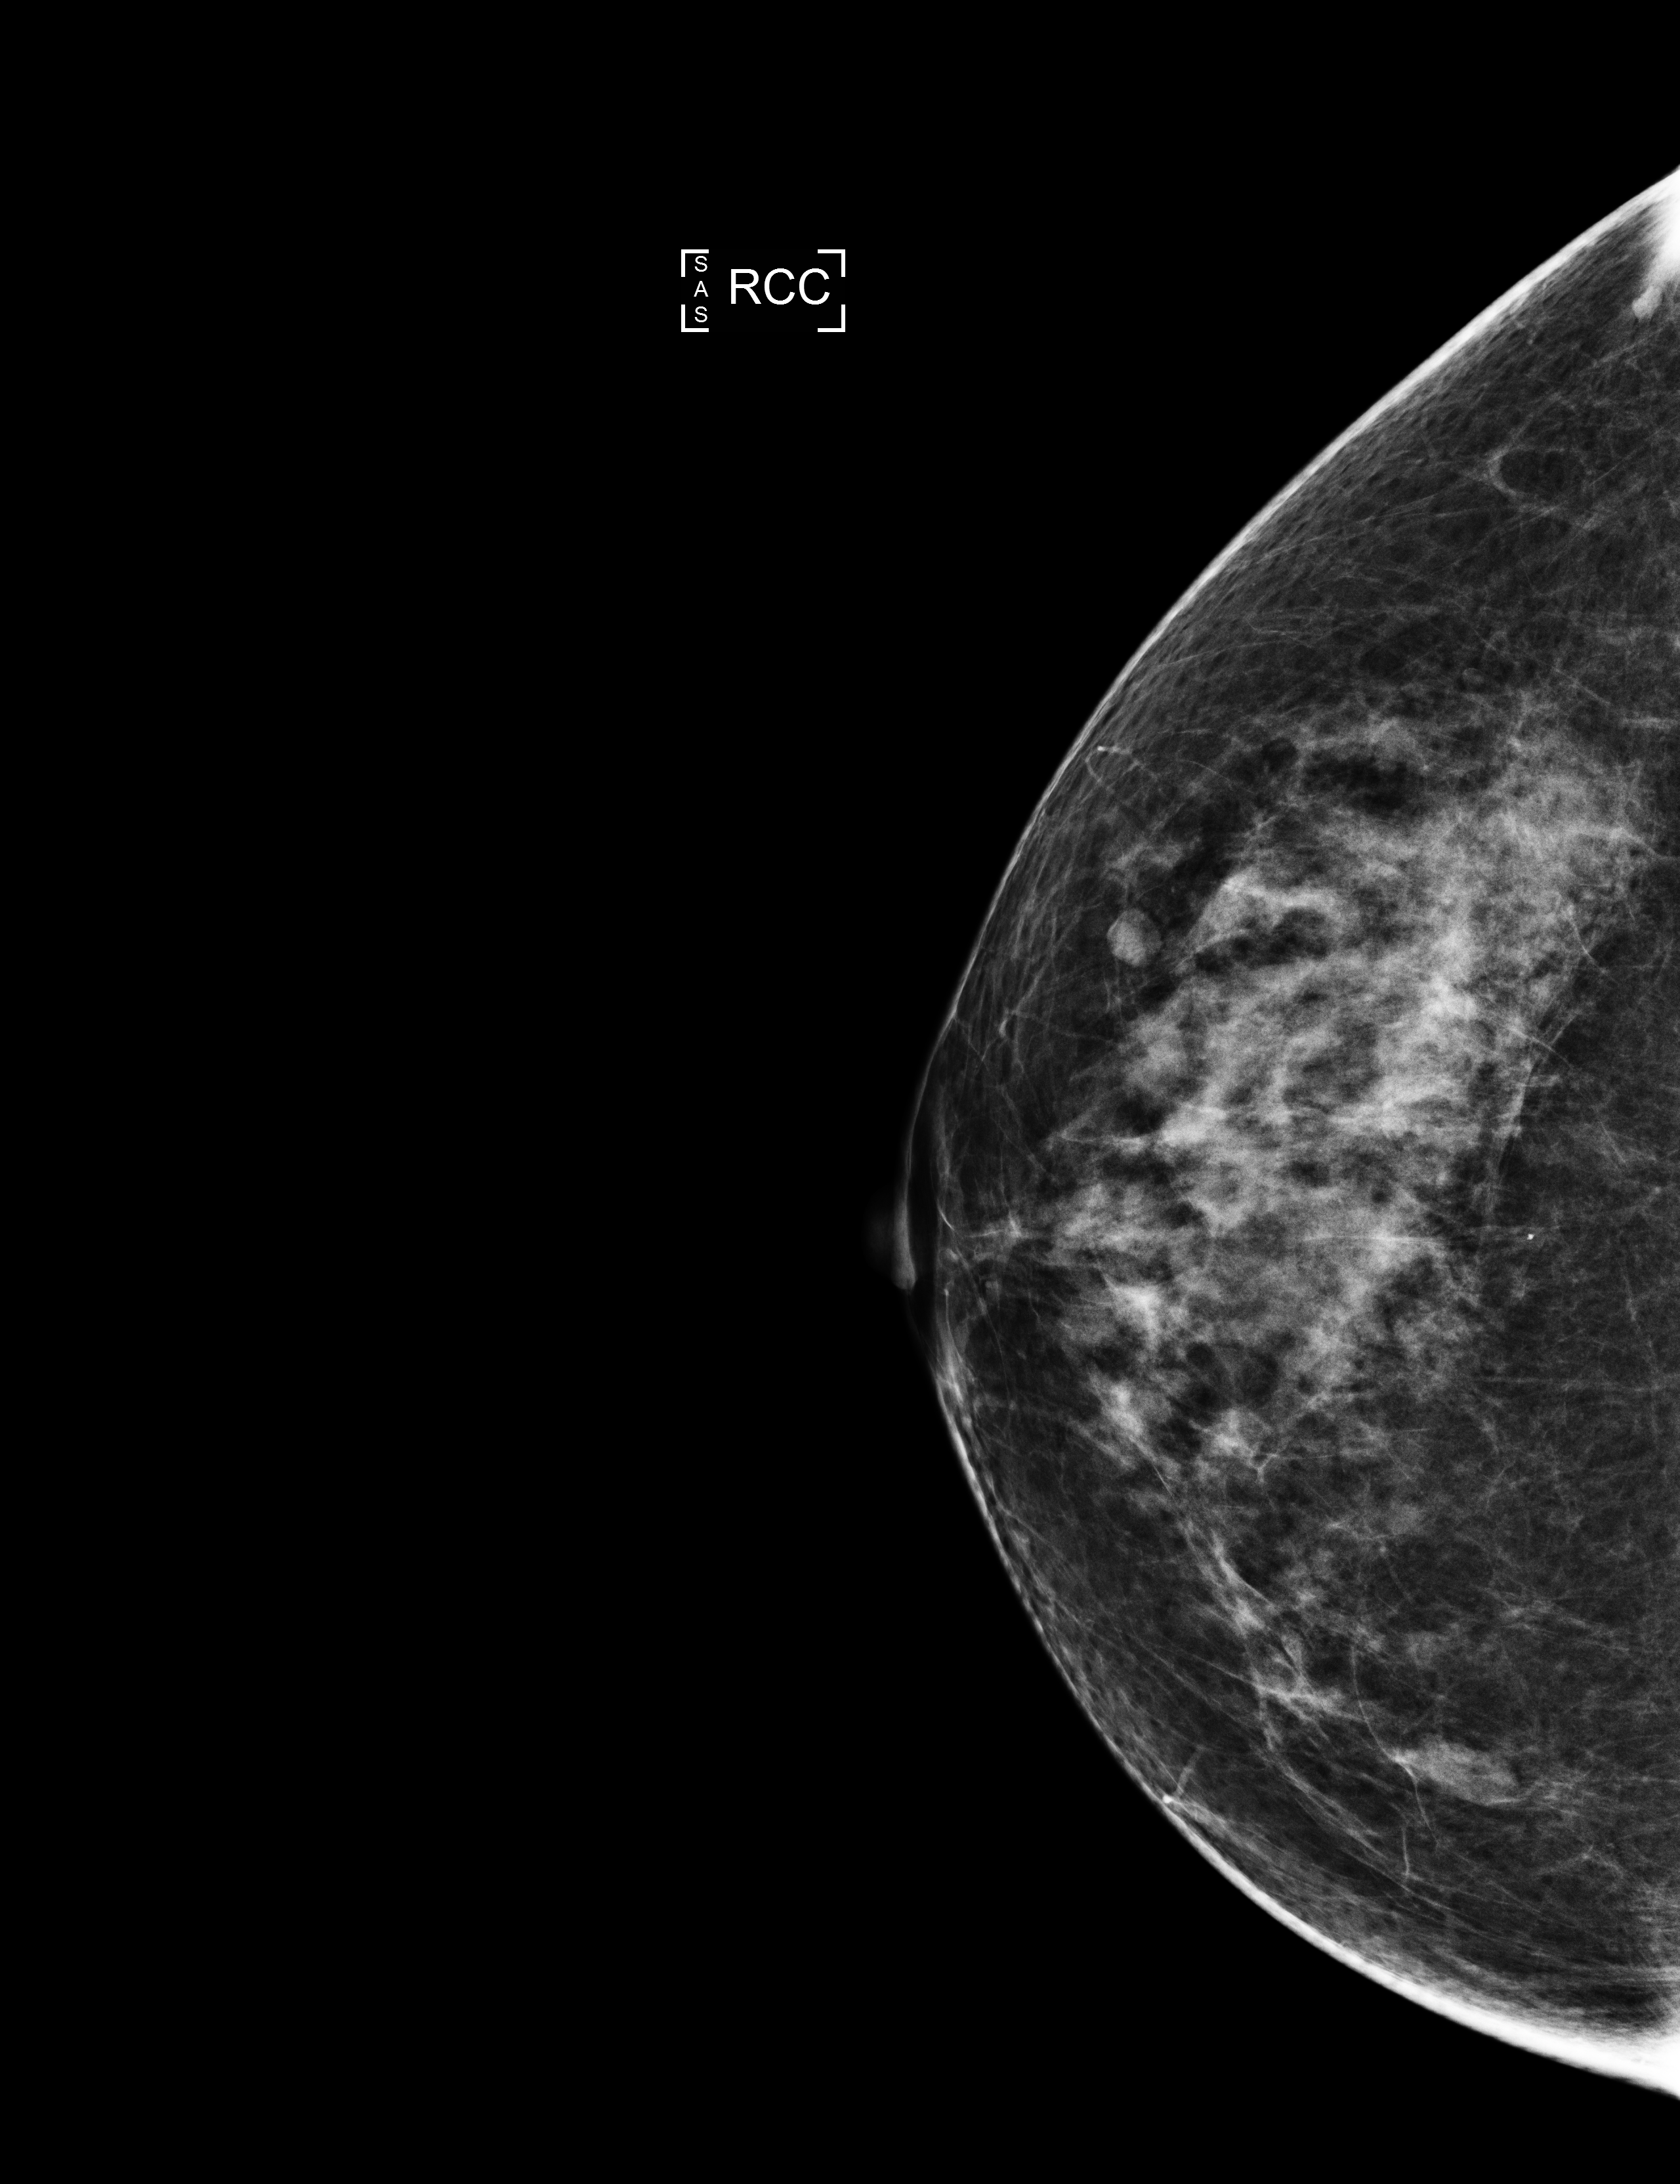
Full-field digital mammogram (FFDM); right breast; cranio-caudal projection; annual screening mammography examination. Female patient, age 54 years.
BI-RADS breast density category at the screening exam (both breasts, scale 1–4): 3. Final BI-RADS category for the screening round (tomosynthesis exam, both breasts): category 1. Recall: no recall after this screen.